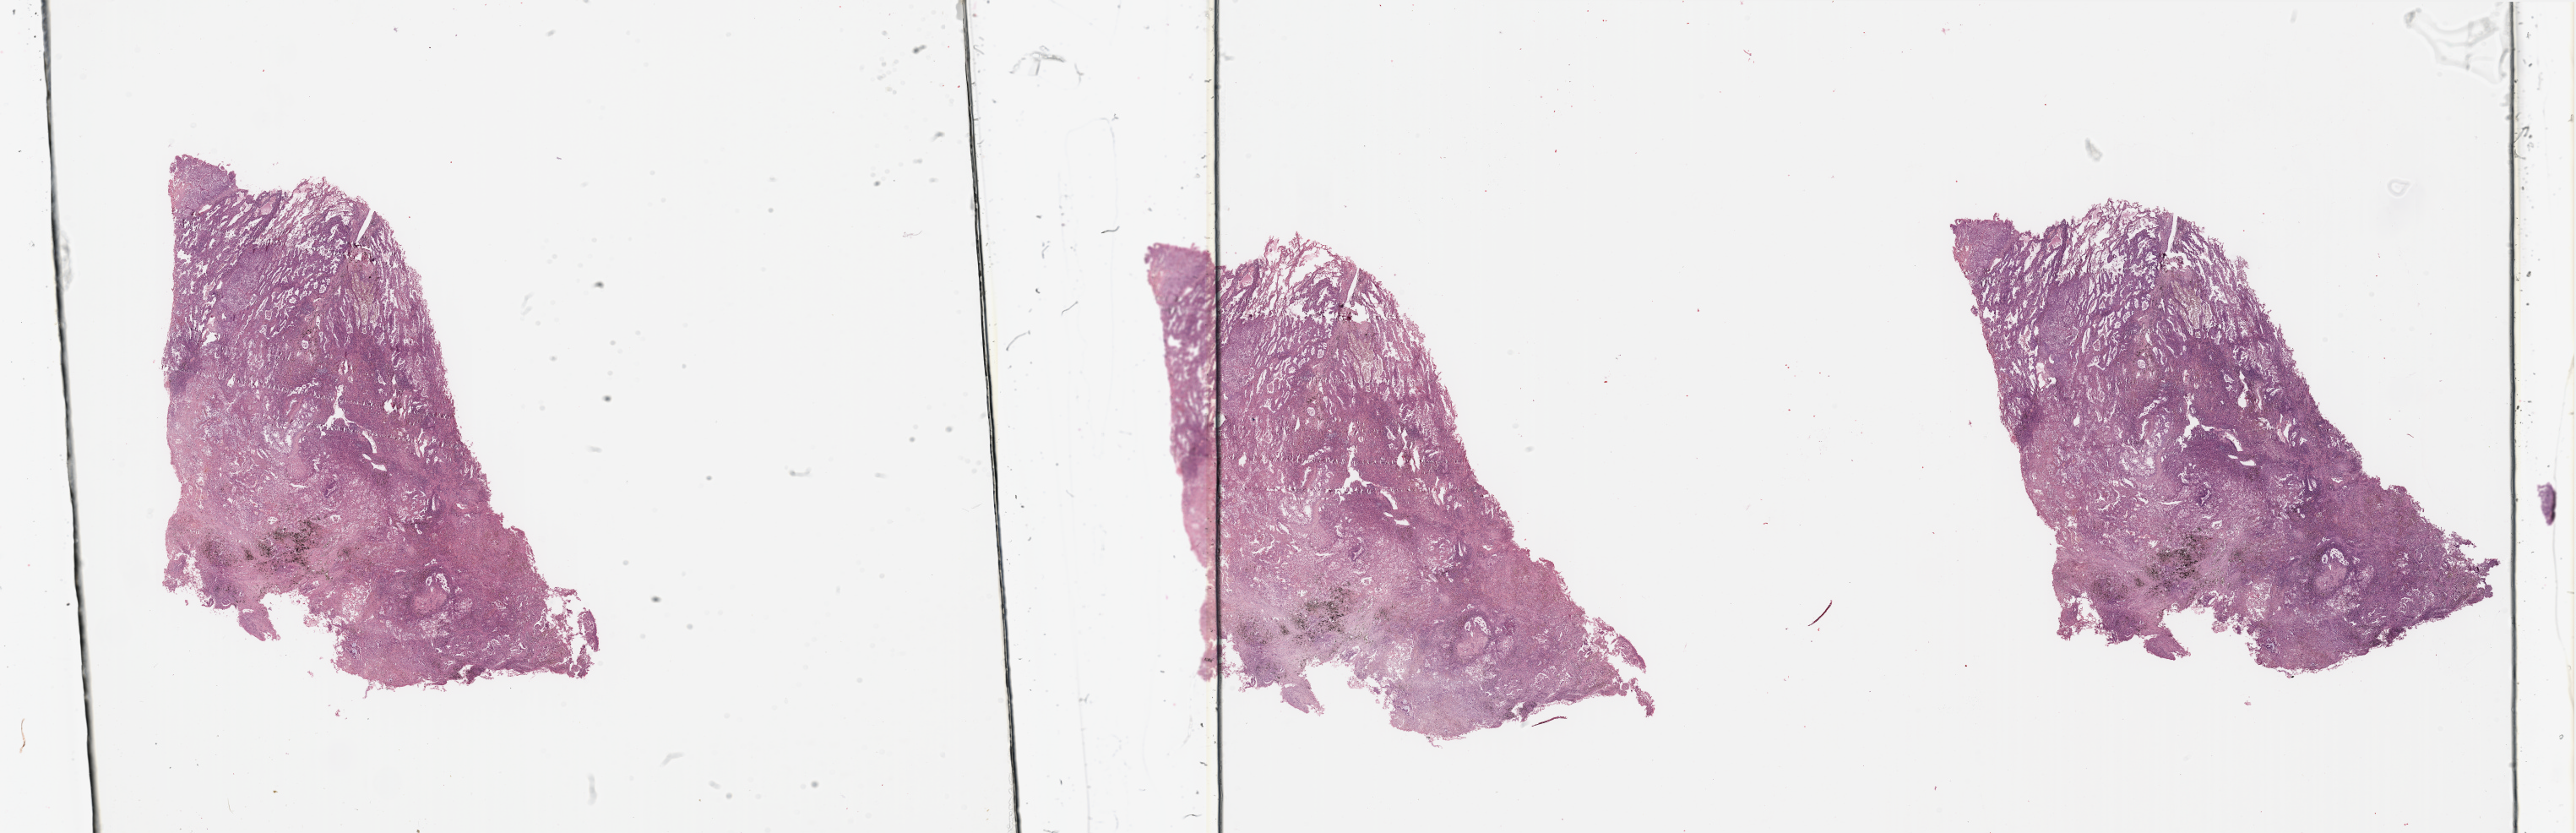
Whole-slide histology image, H&E — shown as a low-resolution overview of the whole scanned area (about 48.2 x 15.6 mm, slide scanned at 20x); tumour tissue sample, sampled site: lung. Male, 51 y/o. Histologic grade: G3 (poorly differentiated). Slide review estimates, as recorded: tumour nuclei 70%, necrosis 7%.
Diagnosis: Adenocarcinoma, NOS. Primary tumour site (as recorded): right lower lobe. AJCC pathologic stage: IB.